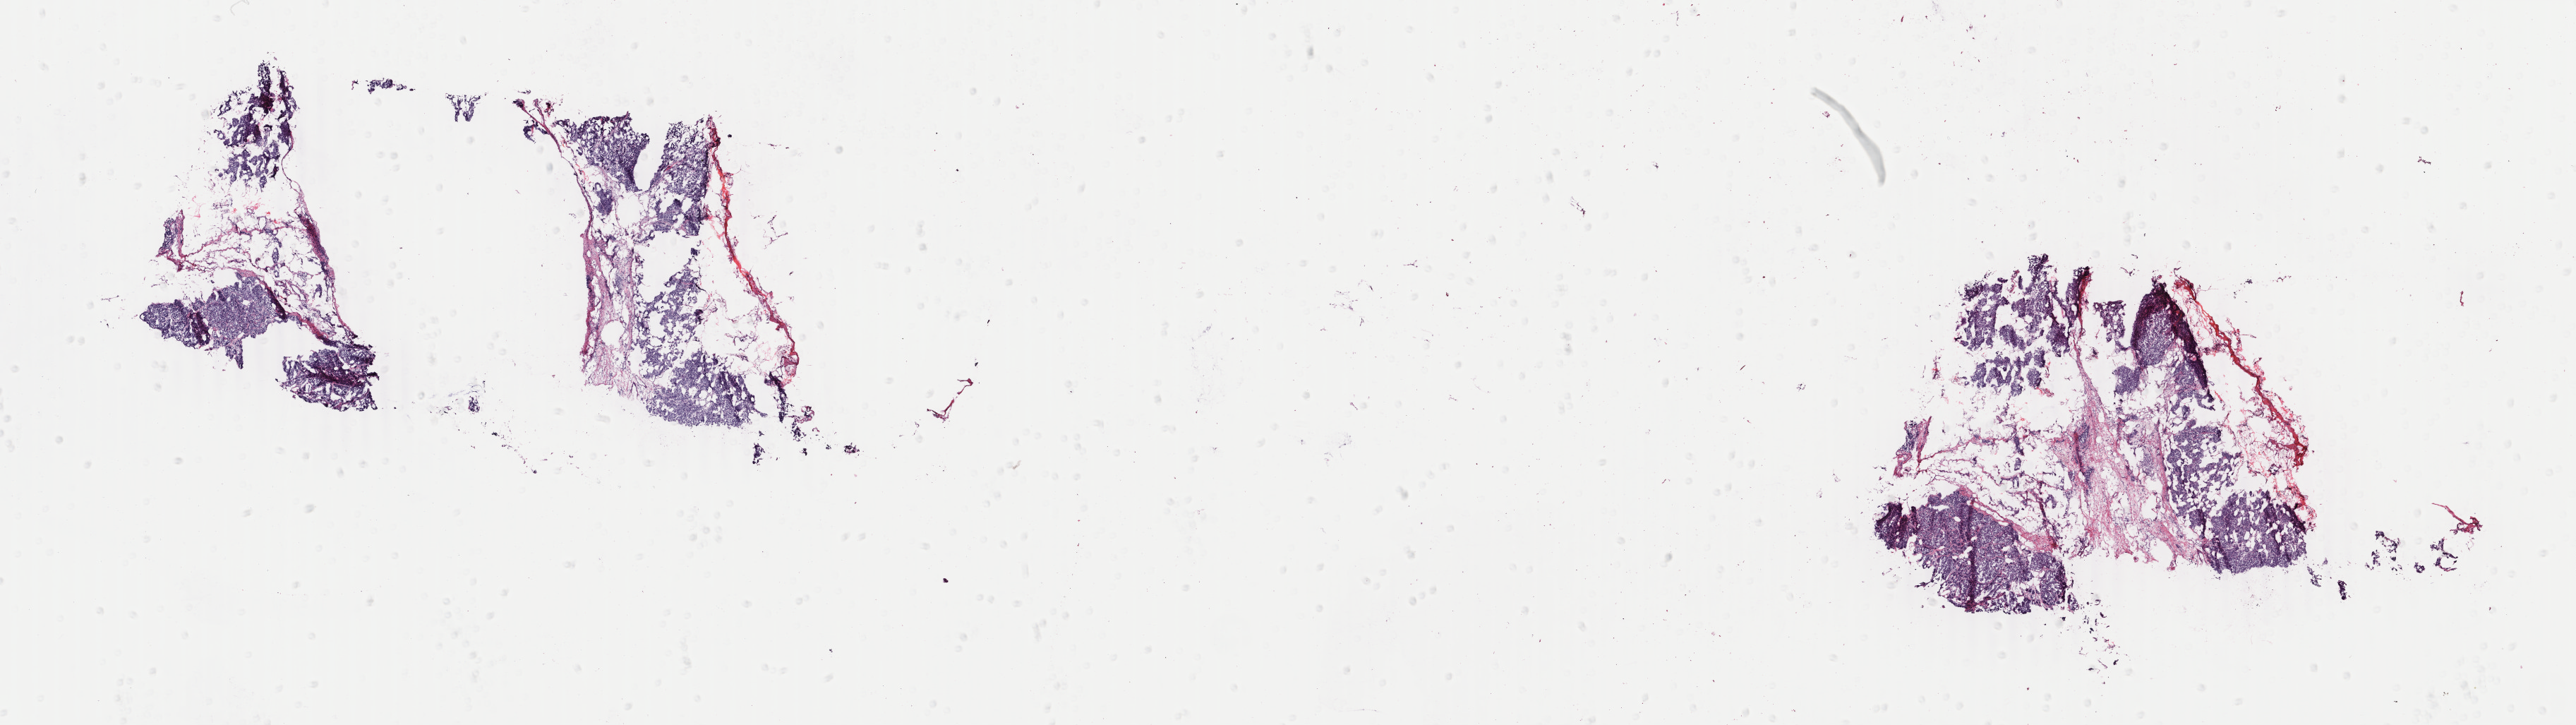
Digitized Hematoxylin and eosin (H&E) stained tissue section (whole slide), low-resolution overview of the scanned area, about 29.0 x 8.2 mm, frozen section, sample: primary tumour, breast. Patient: female, age at initial diagnosis 37 years. Slide review estimates, as recorded: tumour cells 80%, tumour nuclei 80%, normal cells 0%, stromal cells 20%, necrosis 0%. Inflammatory infiltration, as recorded: lymphocyte infiltration 2%, monocyte infiltration 0%, neutrophil infiltration 0%.
- diagnosis: Infiltrating duct carcinoma, NOS
- lymph nodes positive (case pathology): 1 of 23 examined
- AJCC pathologic stage: IIB (6th edition)
- laterality: left